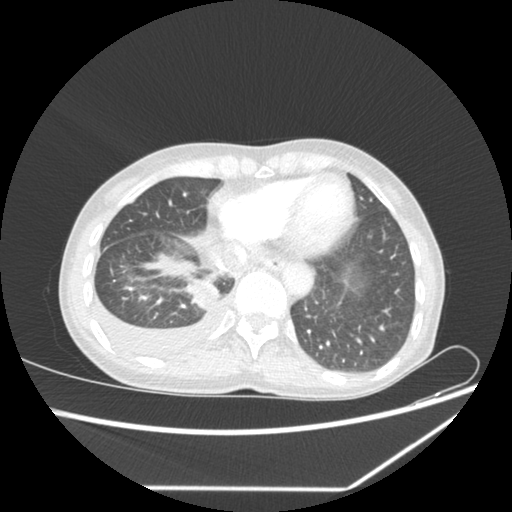
Chest CT, one axial slice; slice 1 of 1 in the series (ordered by position); reconstruction kernel SOFT; 80 kVp; lung window (W 1500 / L -600 HU); 512 × 512 image matrix. Patient: female, 59 years. From the clinical record (not read from this slice): clinical TNM (as recorded): T1c N1 M1.
Outlined on this slice (rectangle marked by the reading radiologist):
- lung tumour (recorded histology: adenocarcinoma): bounding box [x1, y1, x2, y2] px = [185, 275, 222, 312]